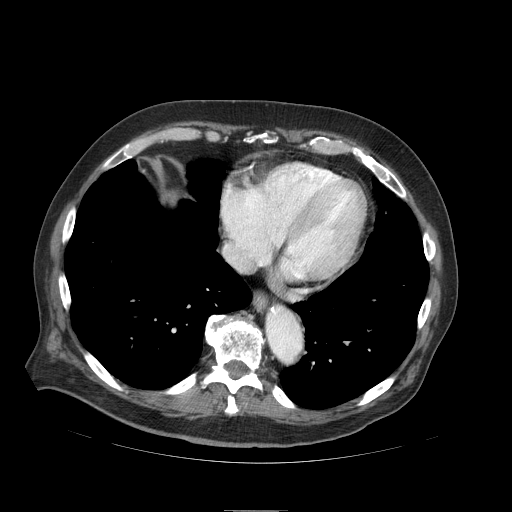
Contrast-enhanced abdominal CT (liver protocol), one axial slice. Slice 88 of 103 in the series (ordered by position). 120 kVp. Soft-tissue window (W 400 / L 40 HU). 512 × 512 image matrix, field of view 440 × 440 mm. Case-level facts recorded for this patient, not image findings: diagnosis: hepatocellular carcinoma (patient treated with transarterial chemoembolisation; whether this scan precedes or follows treatment is not stated here); TNM stage (as recorded): Stage-IIIA.
Annotated regions visible in this slice (semi-automatically segmented with operator editing):
- liver parenchyma outside the tumour (the mass and vessels are separate outlines, so this box may not span the whole liver): bounding box (x1, y1, x2, y2) in pixels: (166, 192, 176, 201)